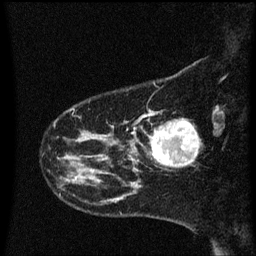
Breast MRI (dynamic contrast-enhanced), one sagittal slice. Dynamic contrast-enhanced series, image 2 of 3 at this slice position (ordered by acquisition). 1.5 T. TE 4.2 ms, TR 8.4 ms. 2 mm slice thickness. 256 × 256 image matrix, field of view 200 × 200 mm. Patient: female, 41 years. Case-level facts recorded for this patient, not image findings: setting: breast cancer imaged before/during neoadjuvant chemotherapy; receptor status: triple-negative.
Annotated regions visible in this slice (semi-automatic segmentation, software-assisted and operator-edited):
- analysis volume of interest (the breast-tissue region the enhancement analysis was run in; not a lesion): bounding box <138,116,198,167> (left, top, right, bottom; pixels)
- tumour enhancement mask (voxels above the 70 % enhancement threshold inside the analysis volume of interest): <151,120,198,167>